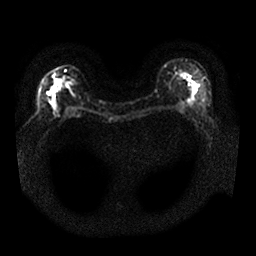
Breast MRI, one axial slice; slice 12 of 25 in the series (ordered by position); diffusion-weighted series; image 2 of 4 stored at this slice position (different b-values; order by instance number); 1.5 T; 4 mm slice thickness; 256 × 256 image matrix. Female patient.
Annotated regions visible in this slice (outlined manually by an expert reader):
- tumour on diffusion-weighted imaging: bounding box [x1, y1, x2, y2] px = [51, 78, 65, 105]